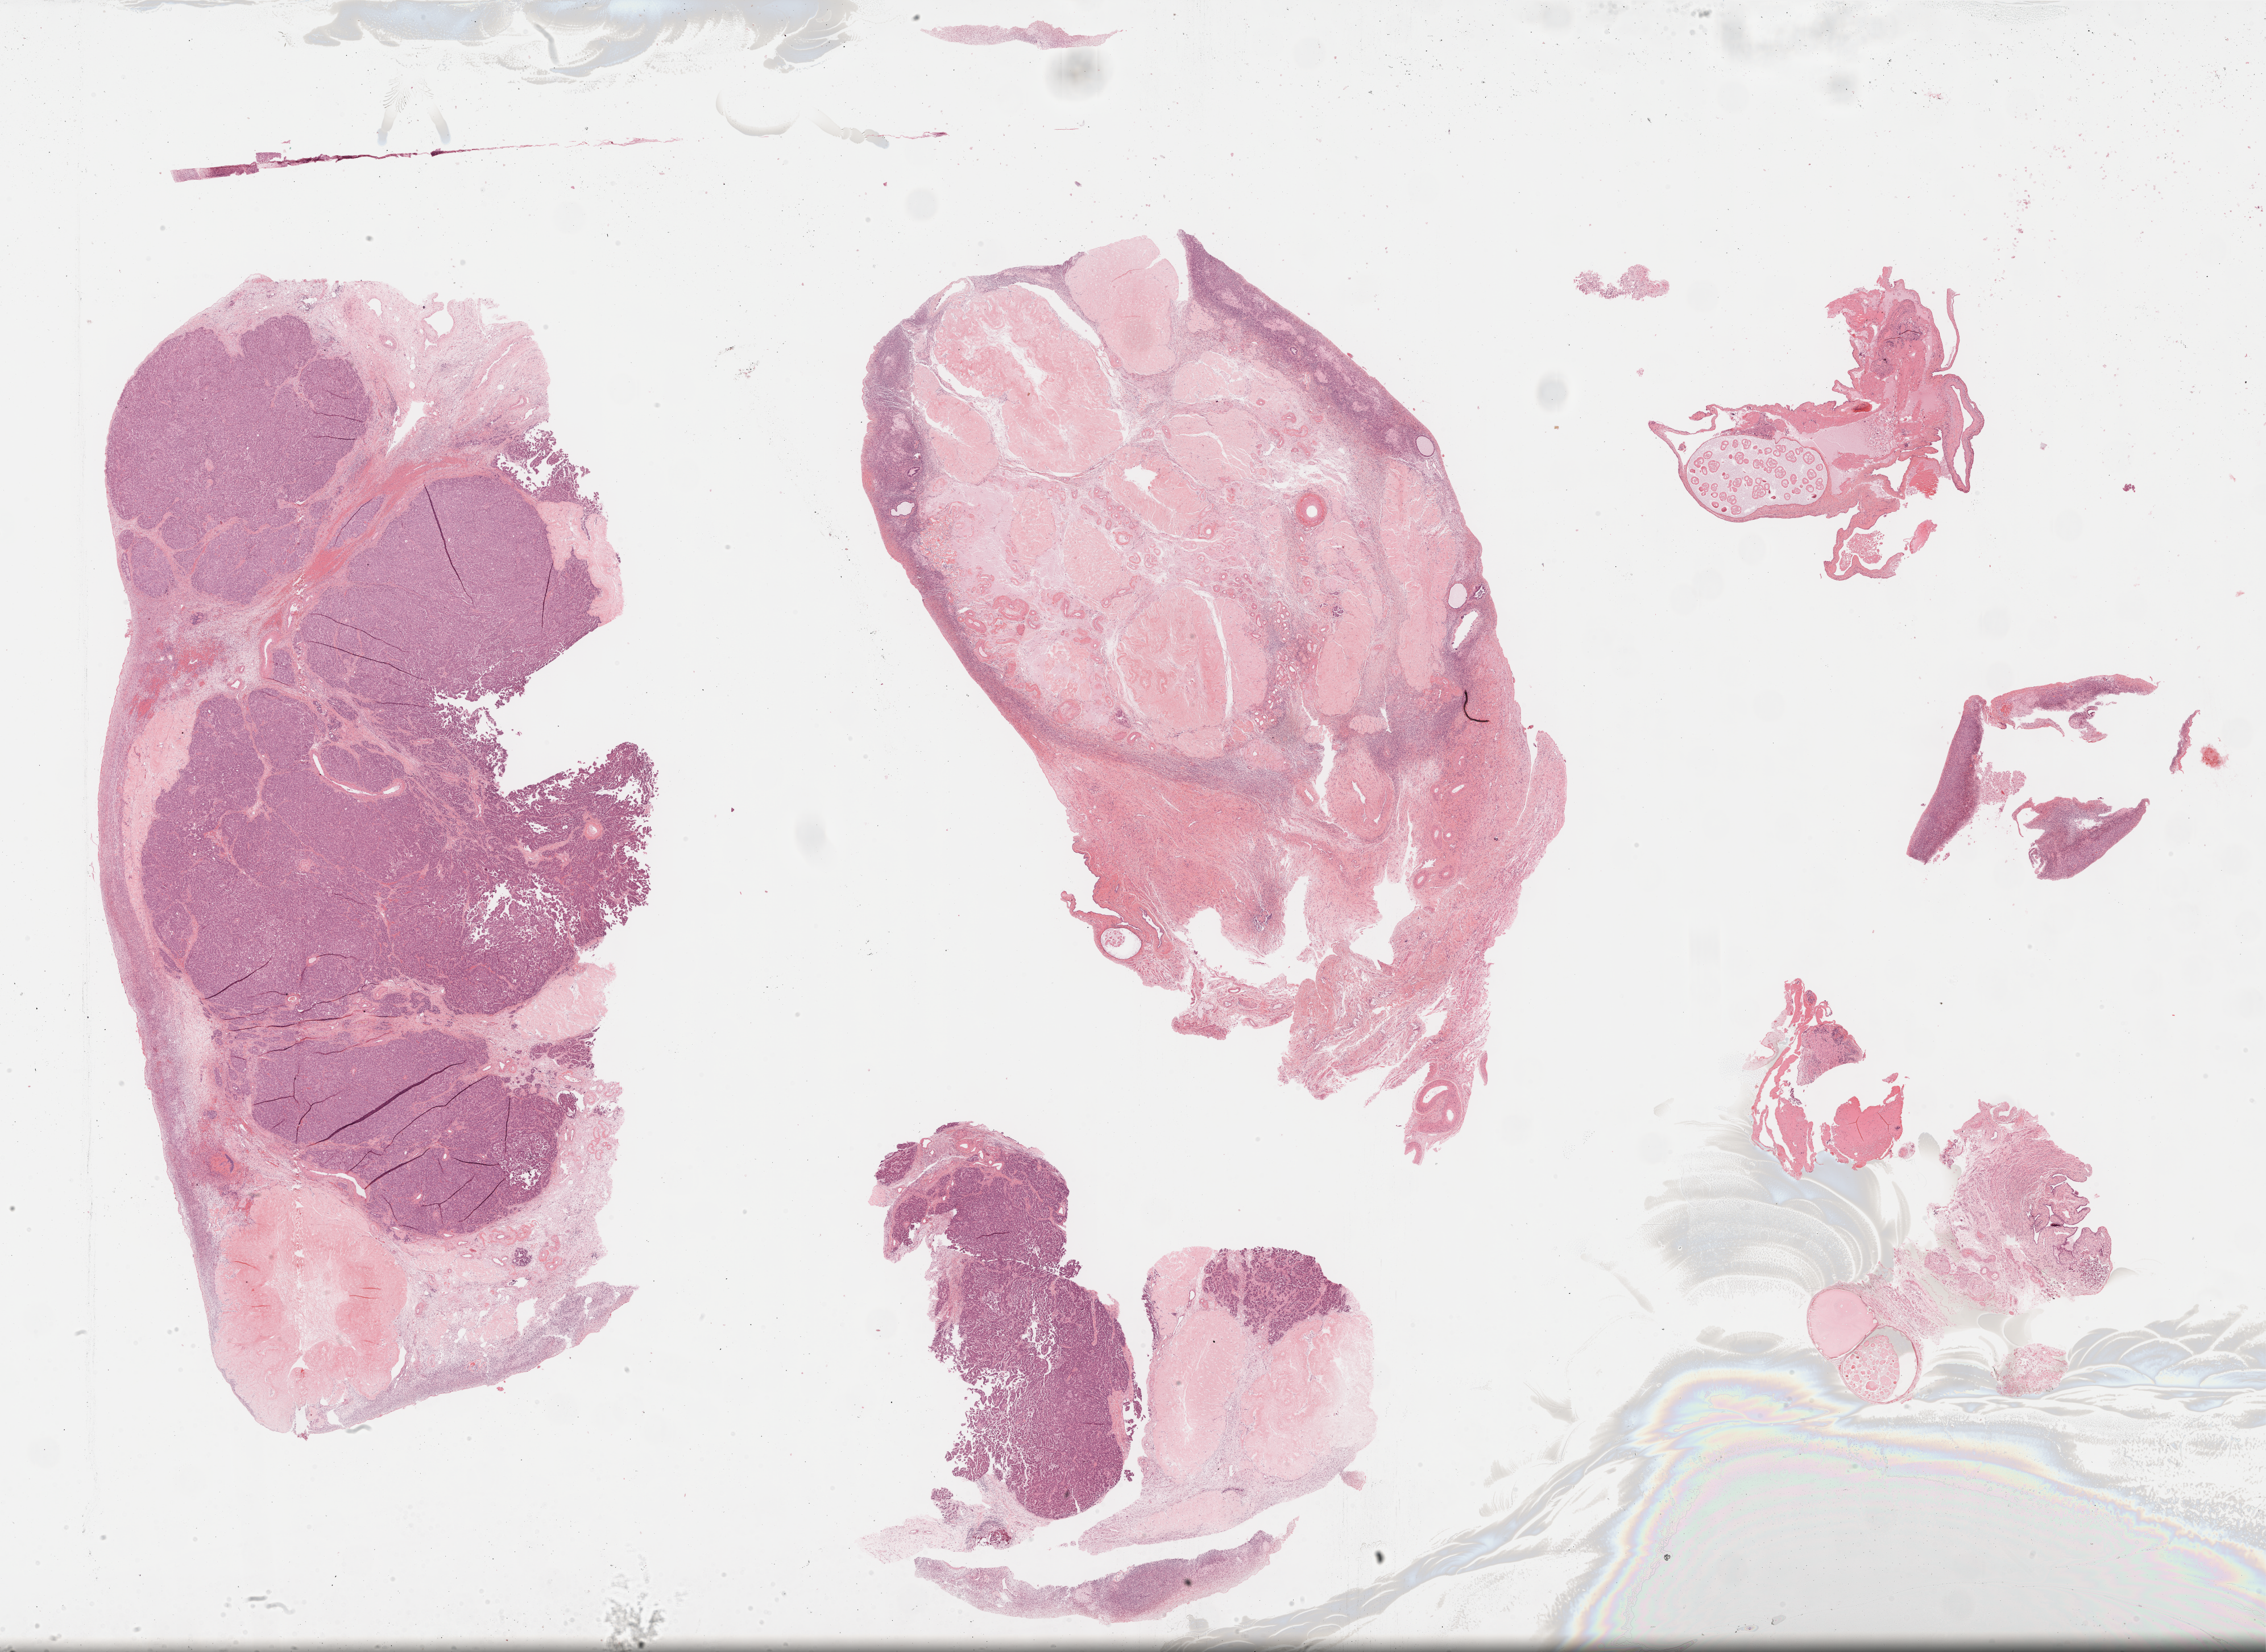
Whole-slide histology image, Hematoxylin and eosin (H&E) stained, shown as a low-resolution overview of the whole scanned area (about 32.2 x 23.5 mm), formalin-fixed paraffin-embedded (FFPE) diagnostic section, primary tumour sample from the ovary. Patient: female, age at initial diagnosis 77 years. Histologic grade: G3 (poorly differentiated).
Diagnosis: Serous cystadenocarcinoma, NOS. FIGO stage: IV.